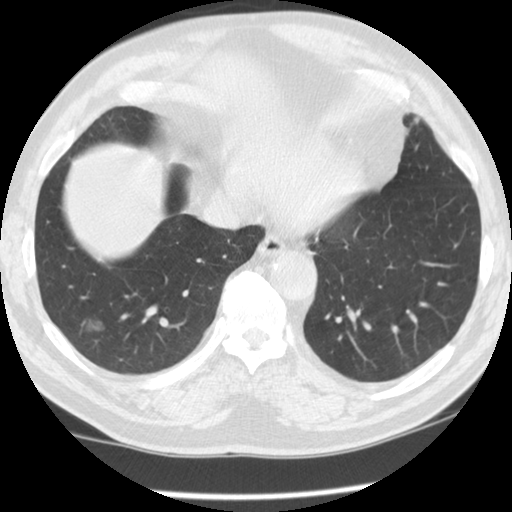
Low-dose screening chest CT, axial slice. Second annual screen. Lung window (W 1500 / L -600 HU). 512 × 512 image matrix. Male participant, aged 62 years at enrolment.
• Expert reader's lesion annotation, box from (x=65, y=303) to (x=131, y=353) px.
• The exam's reader record, not a measurement of the box and not confirmed to be the same lesion: non-calcified nodule or mass ≥4 mm, right lower lobe, 13 × 11 mm, smooth margins, ground glass attenuation, pre-existing on the prior screen: yes; interval growth: no.
• Later outcome: lung cancer diagnosed 330 days after this screen — bronchiolo-alveolar carcinoma, non-mucinous, right lower lobe, well differentiated (G1), stage IA (AJCC 6th edition), 14 mm at pathology.